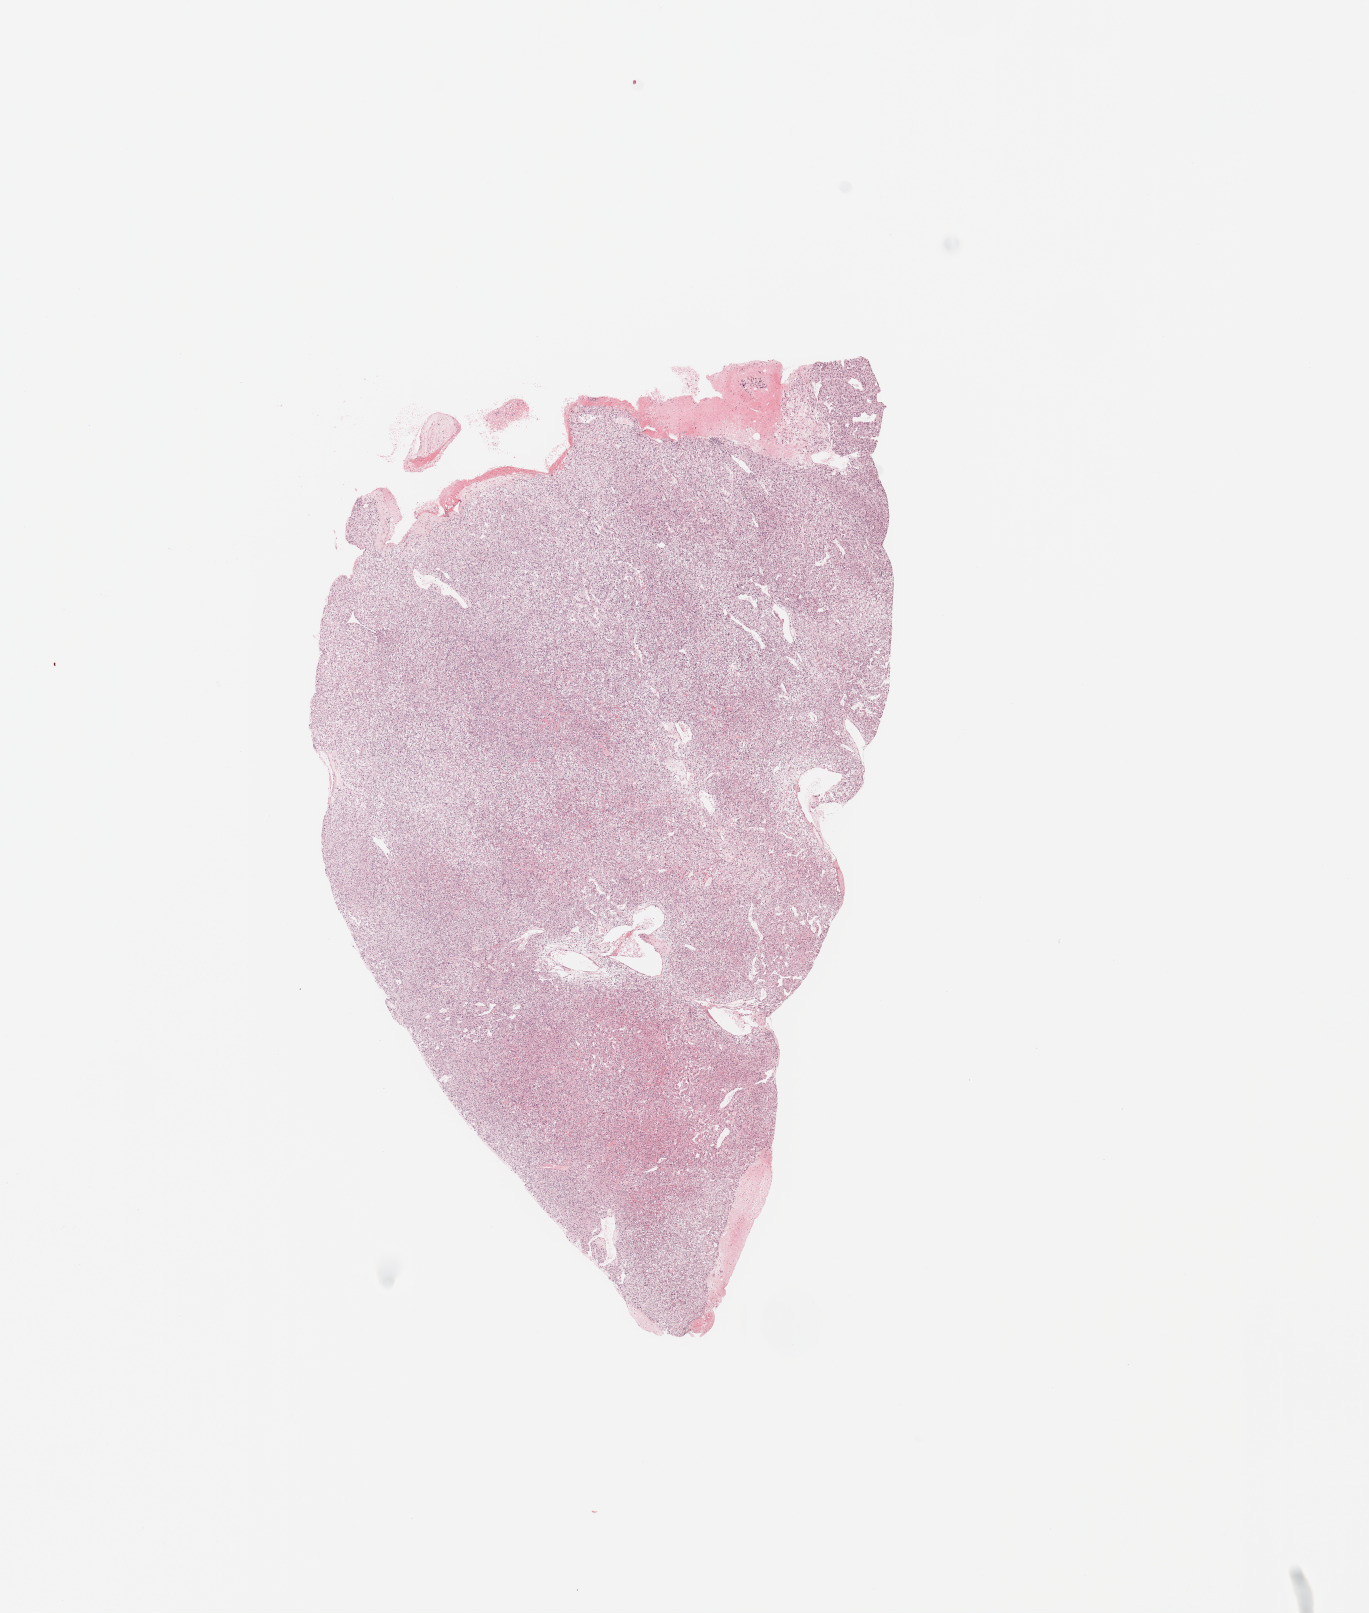
Whole-slide histology image, Hematoxylin and eosin (H&E) stained — a low-resolution overview of the entire scanned area, about 10.8 x 12.8 mm (from a 20x scan); tumour tissue sample, sampled site: kidney. Male, 68 y/o. Histologic grade: G3 (poorly differentiated). Slide review estimates, as recorded: tumour nuclei 90%, necrosis 0%.
• AJCC pathologic stage: III
• histologic diagnosis: Renal cell carcinoma, NOS
• primary tumour site (as recorded): lower pole